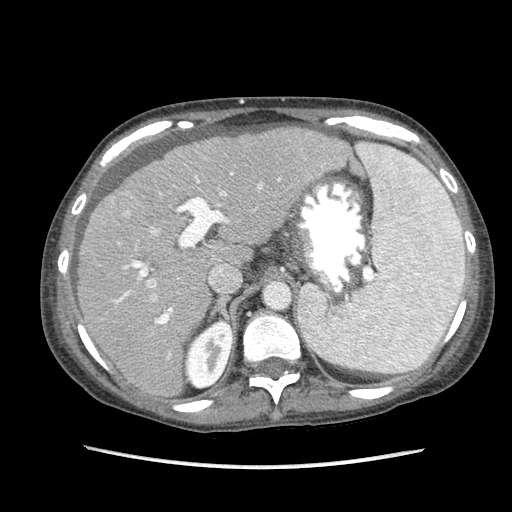
Contrast-enhanced abdominal CT (liver protocol), one axial slice. Slice 60 of 87 in the series (ordered by position). Reconstruction kernel STANDARD. Soft-tissue window (W 400 / L 40 HU). 512 × 512 image matrix, field of view 340 × 340 mm. Case-level facts recorded for this patient, not image findings: diagnosis: hepatocellular carcinoma (patient treated with transarterial chemoembolisation; whether this scan precedes or follows treatment is not stated here); TNM stage (as recorded): Stage-IIIB; Child-Pugh class: A; tumour differentiation: no biopsy.
Structures marked on this image (semi-automatically segmented with operator editing):
- abdominal aorta: box from (x=265, y=284) to (x=289, y=308) px
- liver parenchyma outside the tumour (the mass and vessels are separate outlines, so this box may not span the whole liver): (x=78, y=126)–(x=350, y=396)
- mass: (x=105, y=193)–(x=137, y=219)
- liver vessels: (x=114, y=165)–(x=323, y=358)